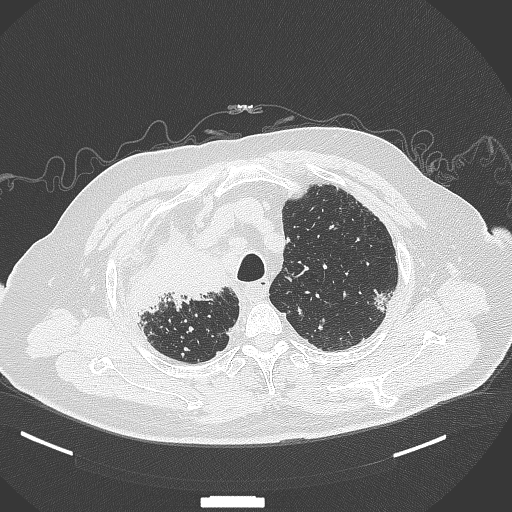
Chest CT, one axial slice; position 294 of 384 along the scan axis; 120 kVp; lung window (W 1500 / L -600 HU); 1 mm slice thickness; 512 × 512 image matrix. Male patient, age 69 years. Case-level facts recorded for this patient, not image findings: clinical TNM (as recorded): T4 N3 M1.
Outlined on this slice (bounding box drawn by a radiologist):
- lung tumour (recorded histology: adenocarcinoma): bounding box [x1, y1, x2, y2] px = [132, 216, 226, 314]